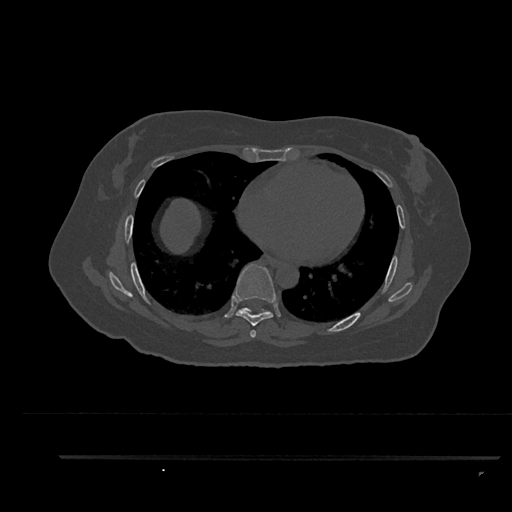
CT including the spine, one axial slice; slice 499 of 797 in the series (ordered by position); reconstruction kernel Br40s/3; bone window (W 1800 / L 400 HU); 512 × 512 image matrix. Patient: female, 44 years. Case-level facts recorded for this patient, not image findings: primary cancer: renal; vertebrae with lytic lesions (as recorded): L1.
Annotated regions visible in this slice (semi-automatically segmented with operator editing):
- T6 vertebra: bounding box (x1, y1, x2, y2) in pixels: (251, 331, 256, 338)
- T7 vertebra: (233, 264, 277, 338)
- T8 vertebra: (237, 308, 270, 315)